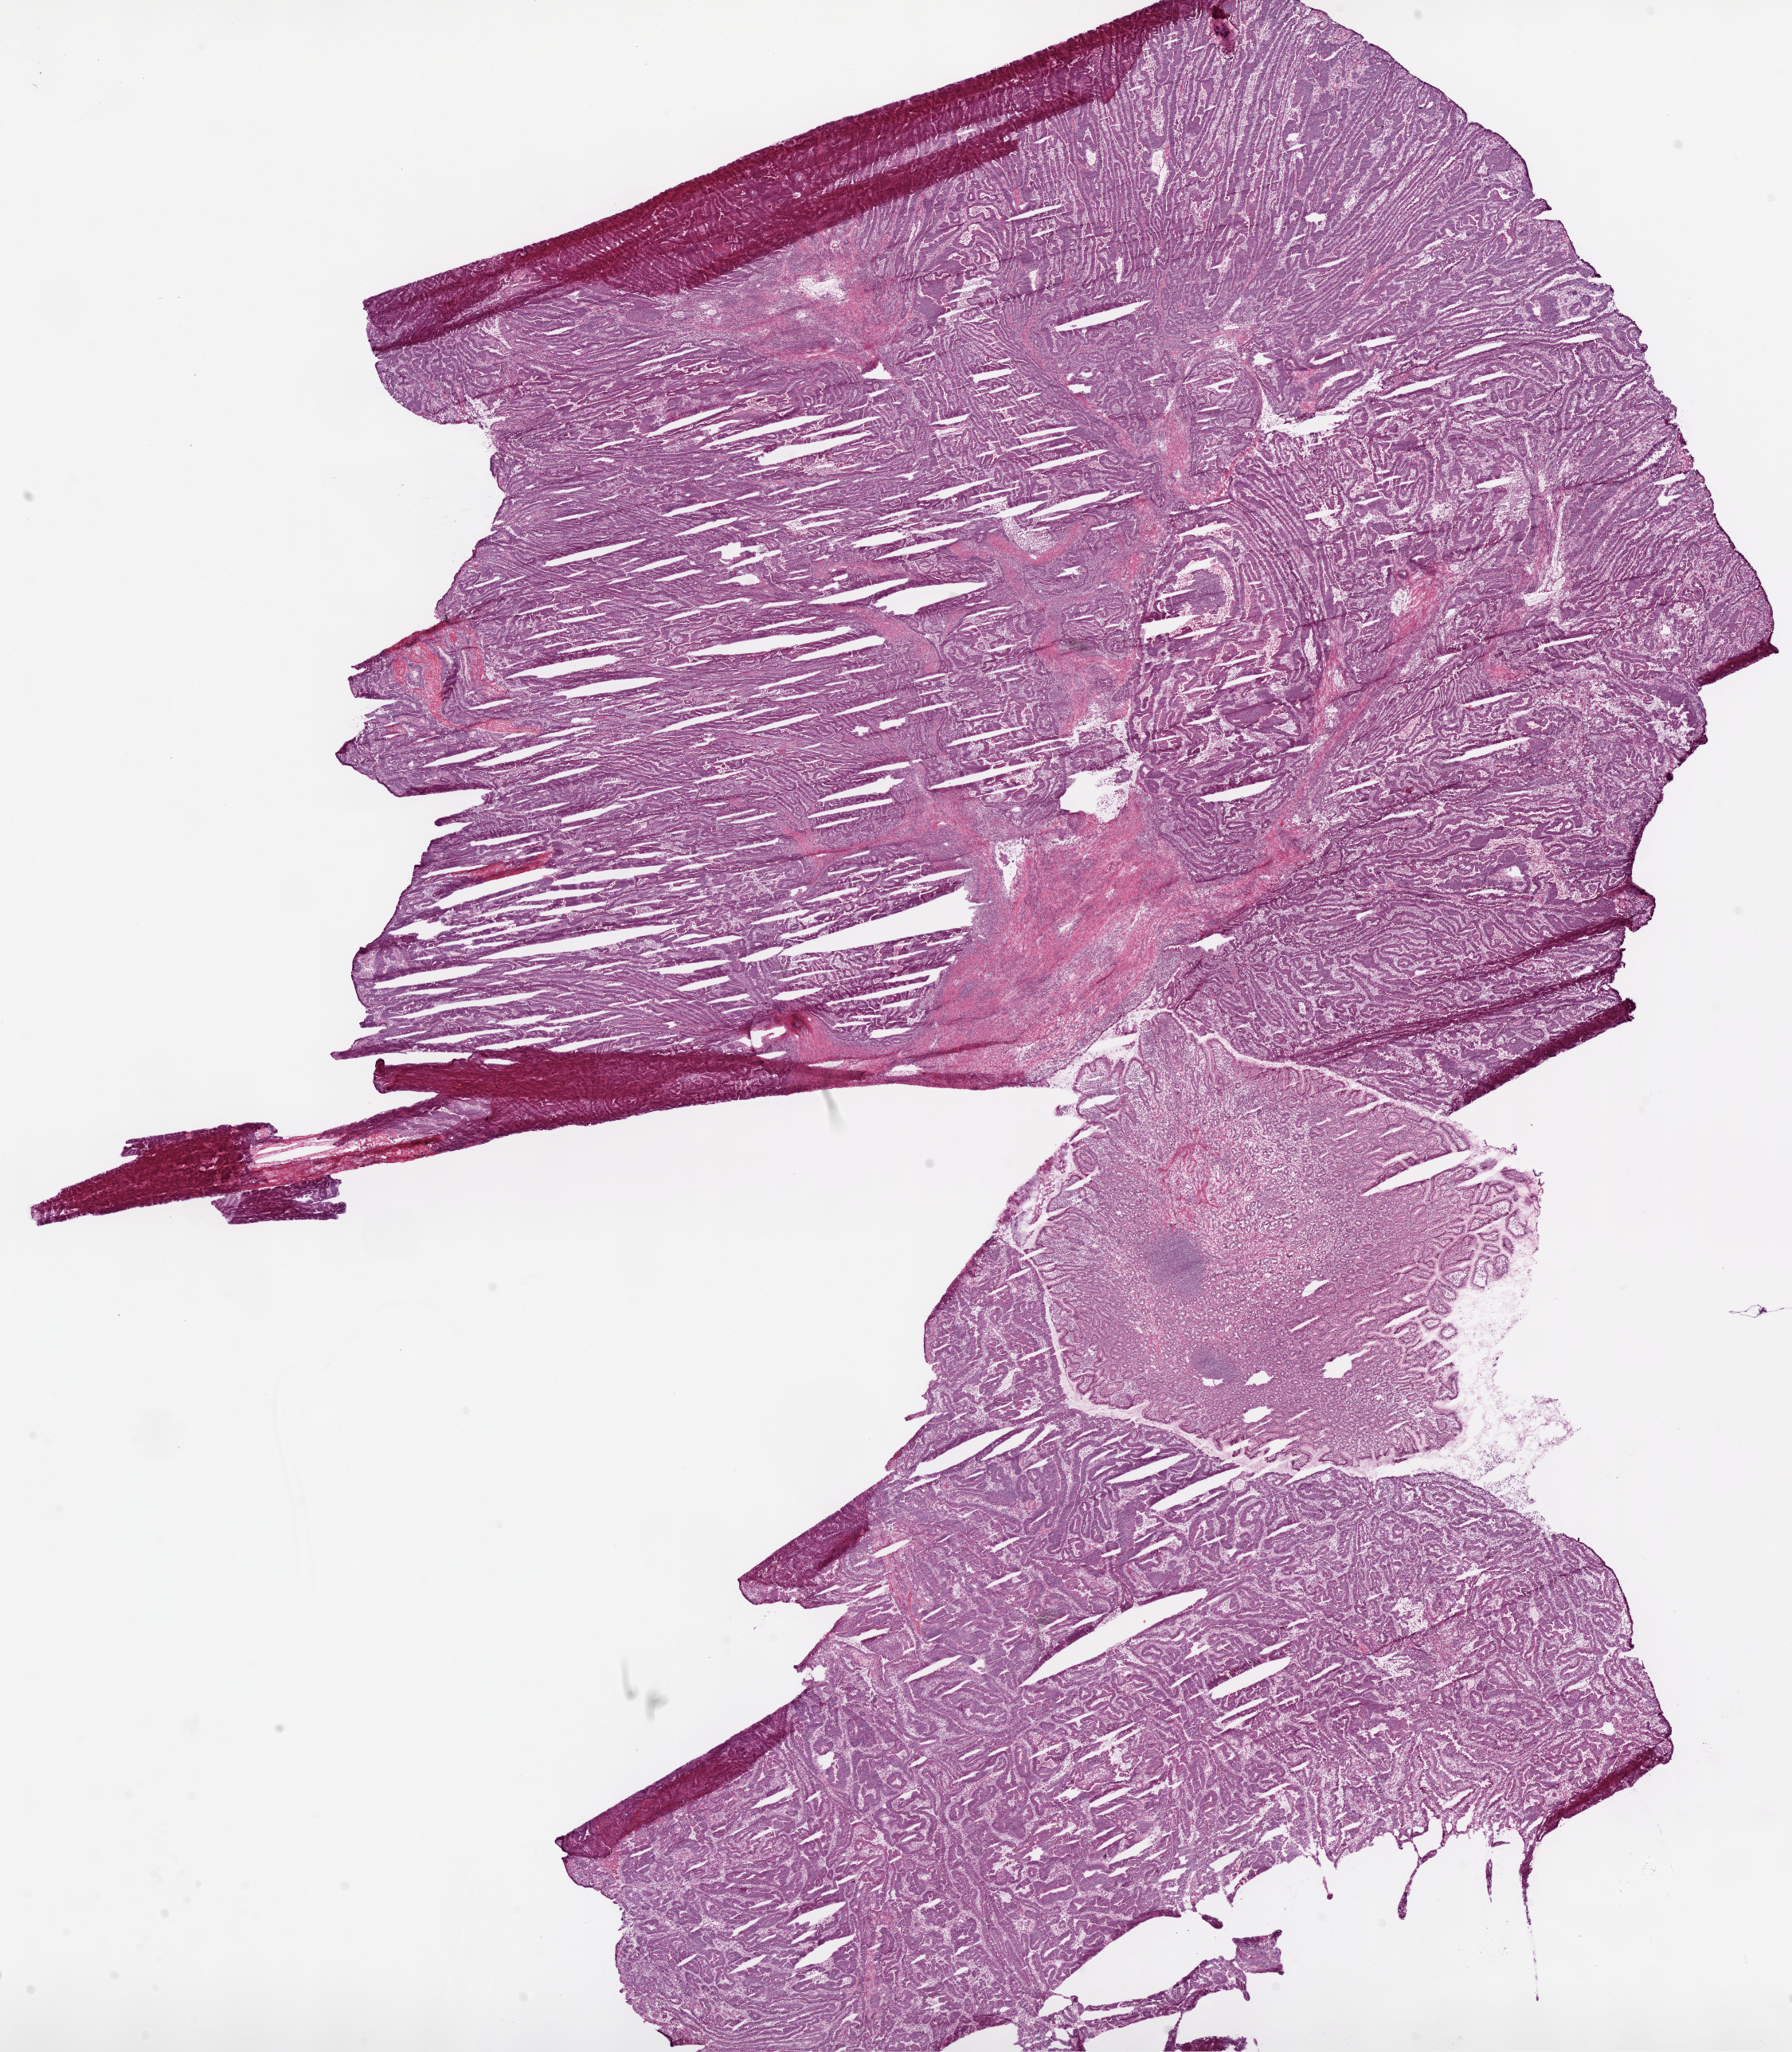
Digitized Hematoxylin and eosin (H&E) stained tissue section (whole slide), shown as a low-resolution overview of the whole scanned area (about 18.1 x 20.7 mm, from a 20x scan). Frozen section. Sample: primary tumour, stomach. Female patient; age at initial diagnosis 73 years. Histologic grade: G1 (well differentiated). Pathologist review of this section (percent, as recorded): tumour cells 80%, tumour nuclei 85%, normal cells 10%, stromal cells 5%, necrosis 5%.
Histologic diagnosis: Adenocarcinoma, NOS (body of stomach).